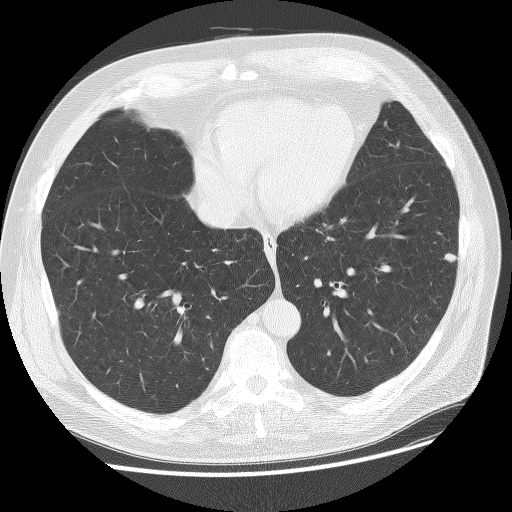
Low-dose screening chest CT, one axial slice. Slice 55 of 137 in the series (ordered by position). Reconstruction kernel BONE. 120 kVp. Lung window (W 1500 / L -600 HU). 2.5 mm slice thickness. 512 × 512 image matrix, field of view 380 × 380 mm.
Structures marked on this image (manually delineated by an expert):
- lesion 4 (tumor): bounding box (x1, y1, x2, y2) in pixels: (444, 253, 457, 262)